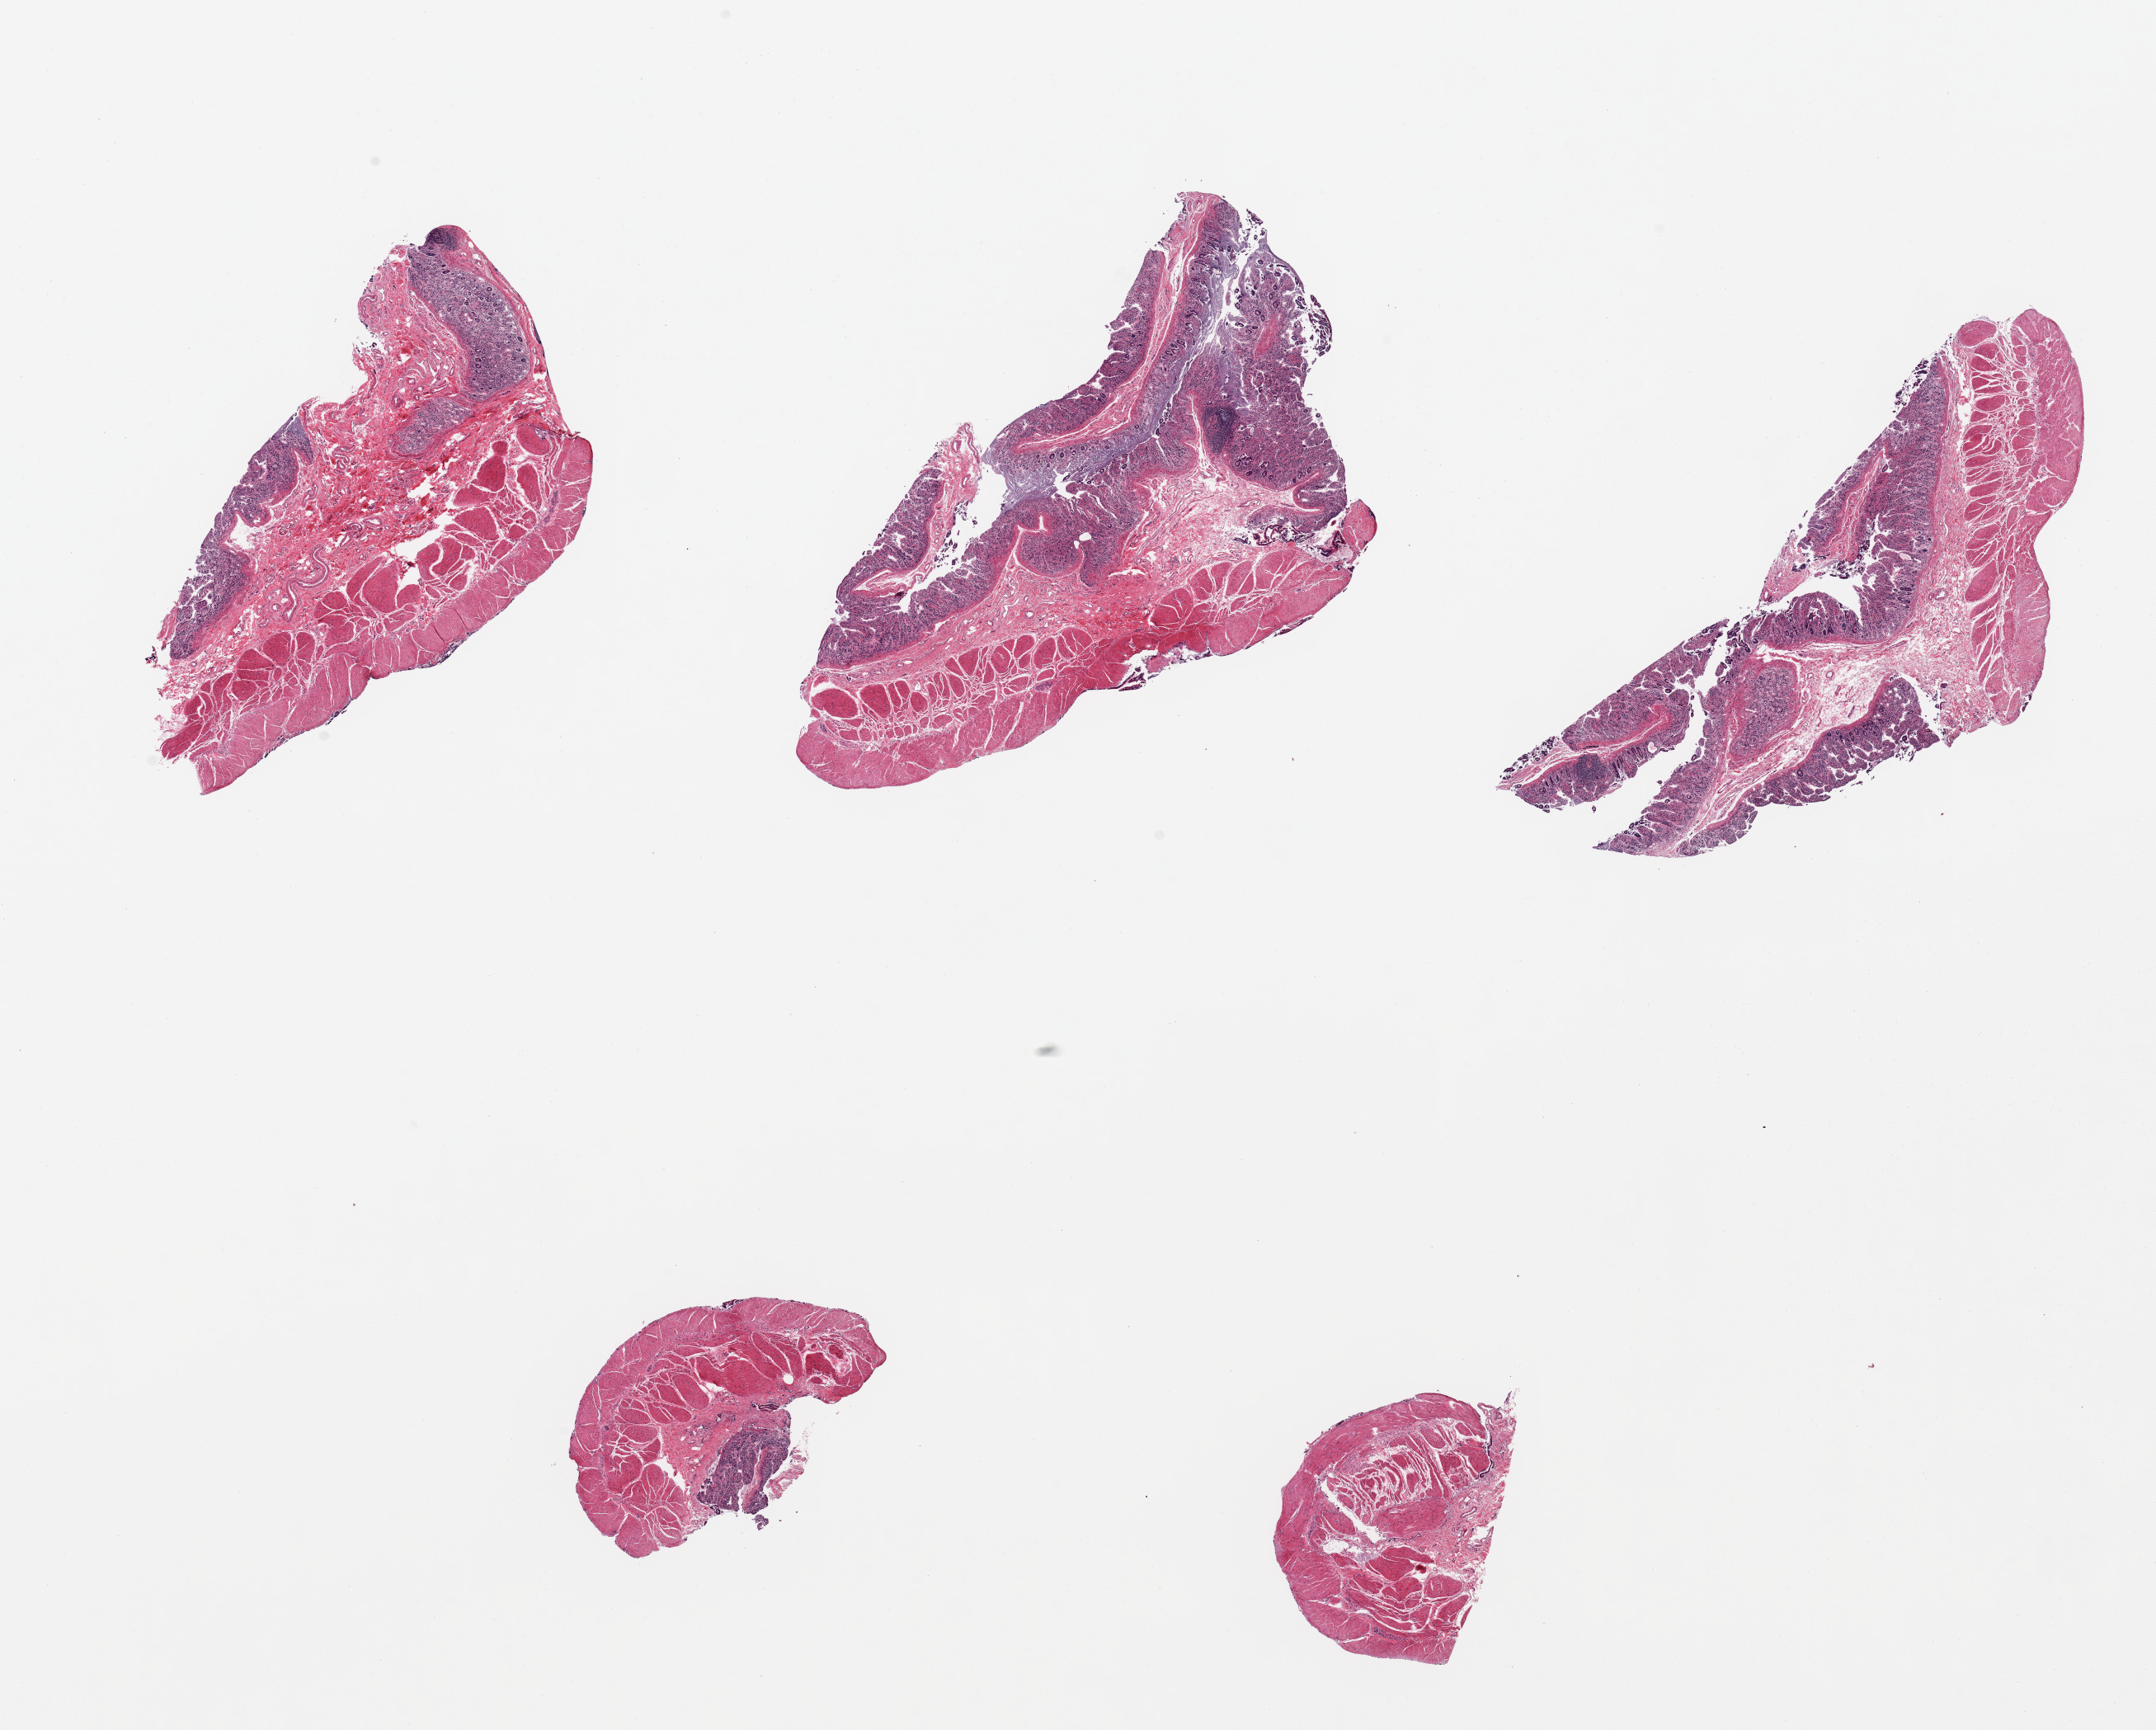
Whole-slide image, haematoxylin and eosin stain, a low-resolution overview of the entire scanned area, about 20.7 x 16.6 mm; PAXgene-fixed paraffin-embedded (PFPE) section; target tissue: transverse colon; tissue donor sample.
Pathologist's review note for this sample: 5 pieces; mucosa autolyzed; muscle intact.